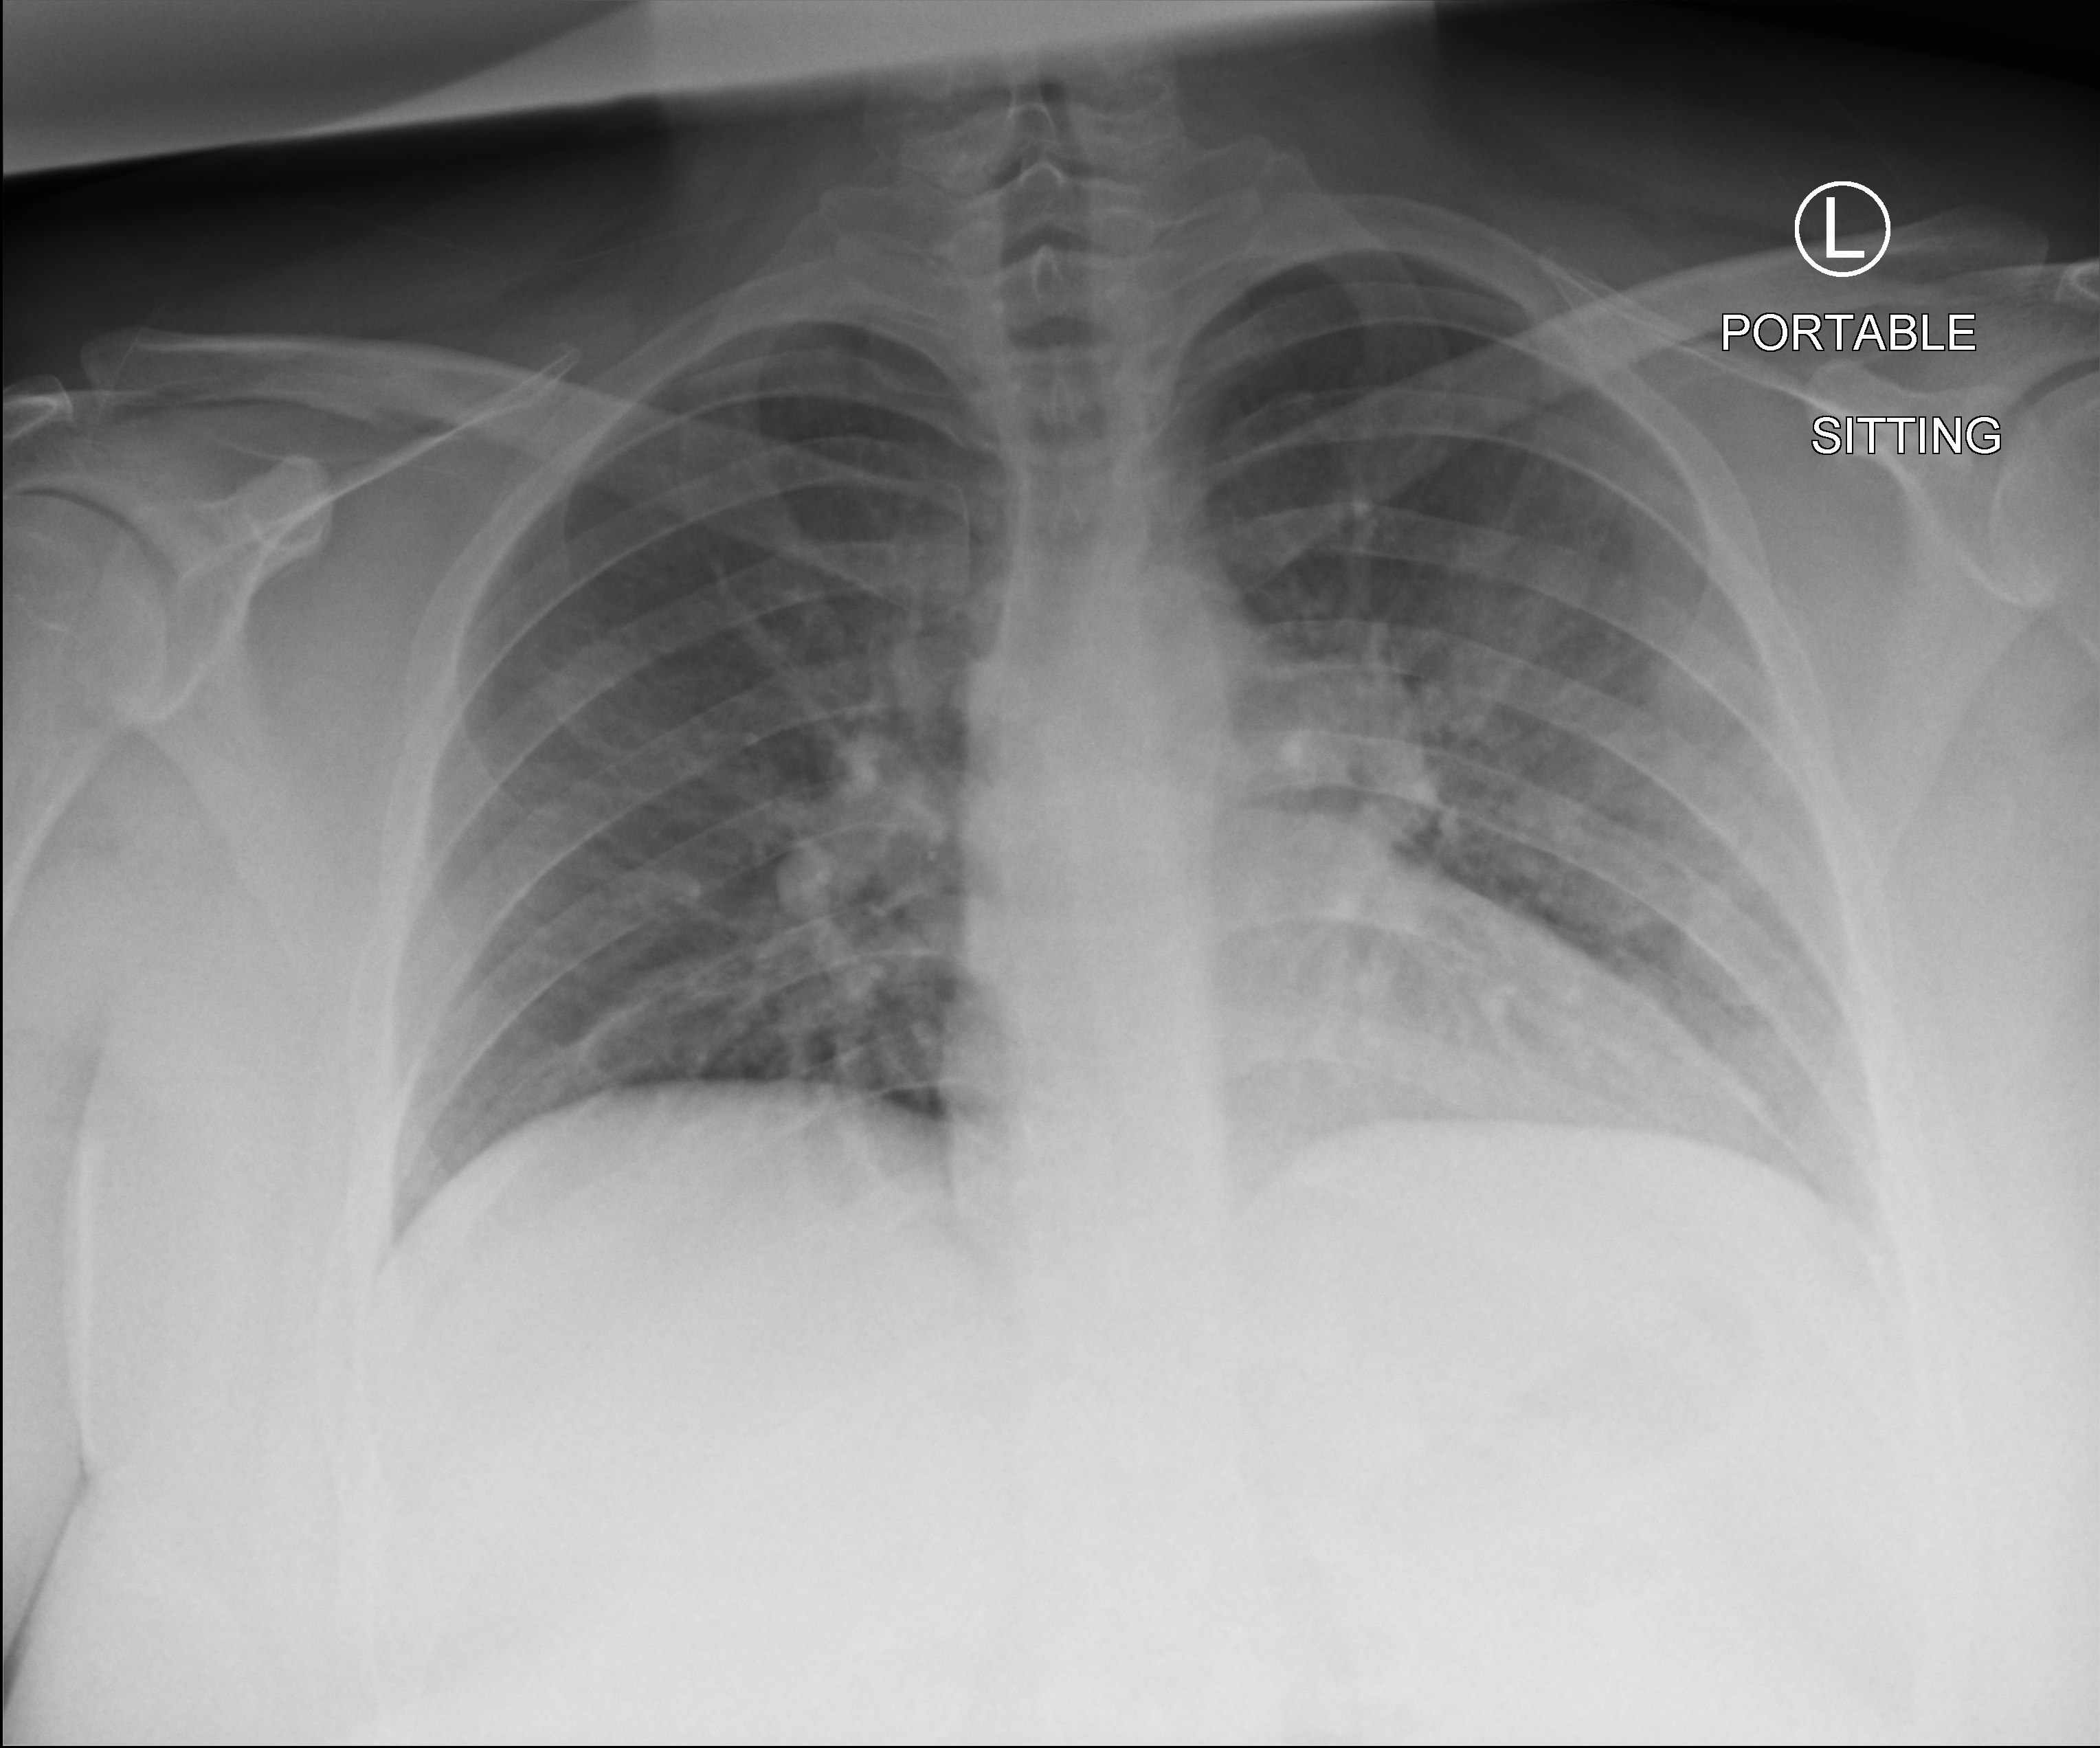
Bedside chest radiograph (computed radiography), anteroposterior (AP) projection. Patient hospitalised with COVID-19; female, aged 18–59 years.
Admission-level facts for this patient (not findings on this image; timing relative to this image not recorded): mechanically ventilated during this hospital stay: no.